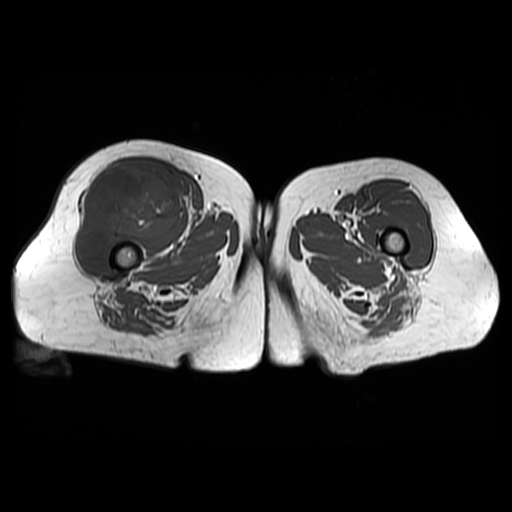
MRI of an extremity soft-tissue mass, one axial slice. Slice 33 of 48 in the series (ordered by position). 512 × 512 image matrix, field of view 440 × 440 mm. Female patient. Case-level facts recorded for this patient, not image findings: histological type: pleiomorphic undifferentiated sarcoma; grade: high; site of the primary tumour: right quadricep.
Outlined on this slice (outlined manually by an expert reader):
- gross tumour volume including surrounding oedema: bounding box <76,164,181,266> (left, top, right, bottom; pixels)
- gross tumour volume (mass): <76,164,181,266>